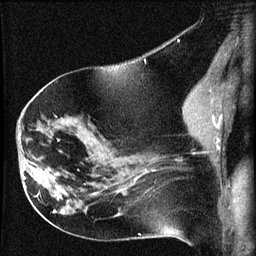
Breast MRI (dynamic contrast-enhanced), one sagittal slice. Slice 35 of 60 in the series (ordered by position). Dynamic contrast-enhanced series, image 2 of 3 at this slice position (ordered by acquisition). 1.5 T. TE 4.2 ms, TR 8.2 ms. 2 mm slice thickness. 256 × 256 image matrix, field of view 180 × 180 mm. Patient: female, 63 years.
Annotated regions visible in this slice (semi-automatic segmentation, software-assisted and operator-edited):
- analysis volume of interest (the breast-tissue region the enhancement analysis was run in; not a lesion): bounding box [x1, y1, x2, y2] px = [22, 156, 64, 202]
- tumour enhancement mask (voxels above the 70 % enhancement threshold inside the analysis volume of interest): [23, 165, 64, 199]